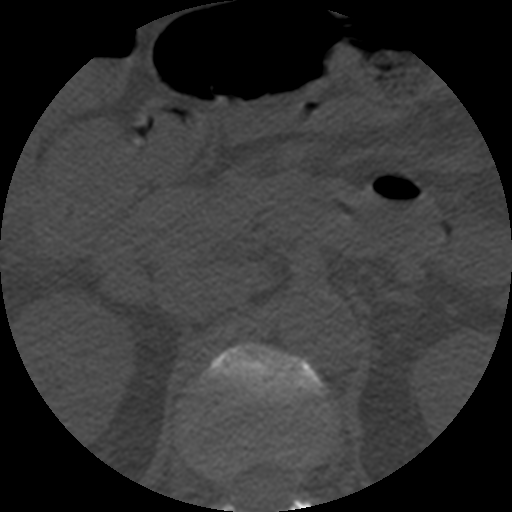
CT including the spine, one axial slice; position 199 of 508 along the scan axis; reconstruction kernel STANDARD; 120 kVp; bone window (W 1800 / L 400 HU); 1.25 mm slice thickness; 512 × 512 image matrix, field of view 160 × 160 mm. Patient age 57 years. Case-level facts recorded for this patient, not image findings: primary cancer: prostate.
Annotated regions visible in this slice (semi-automatic segmentation, software-assisted and operator-edited):
- L1 vertebra: bounding box (x1, y1, x2, y2) in pixels: (205, 344, 326, 512)
- T12 vertebra: (241, 452, 284, 460)